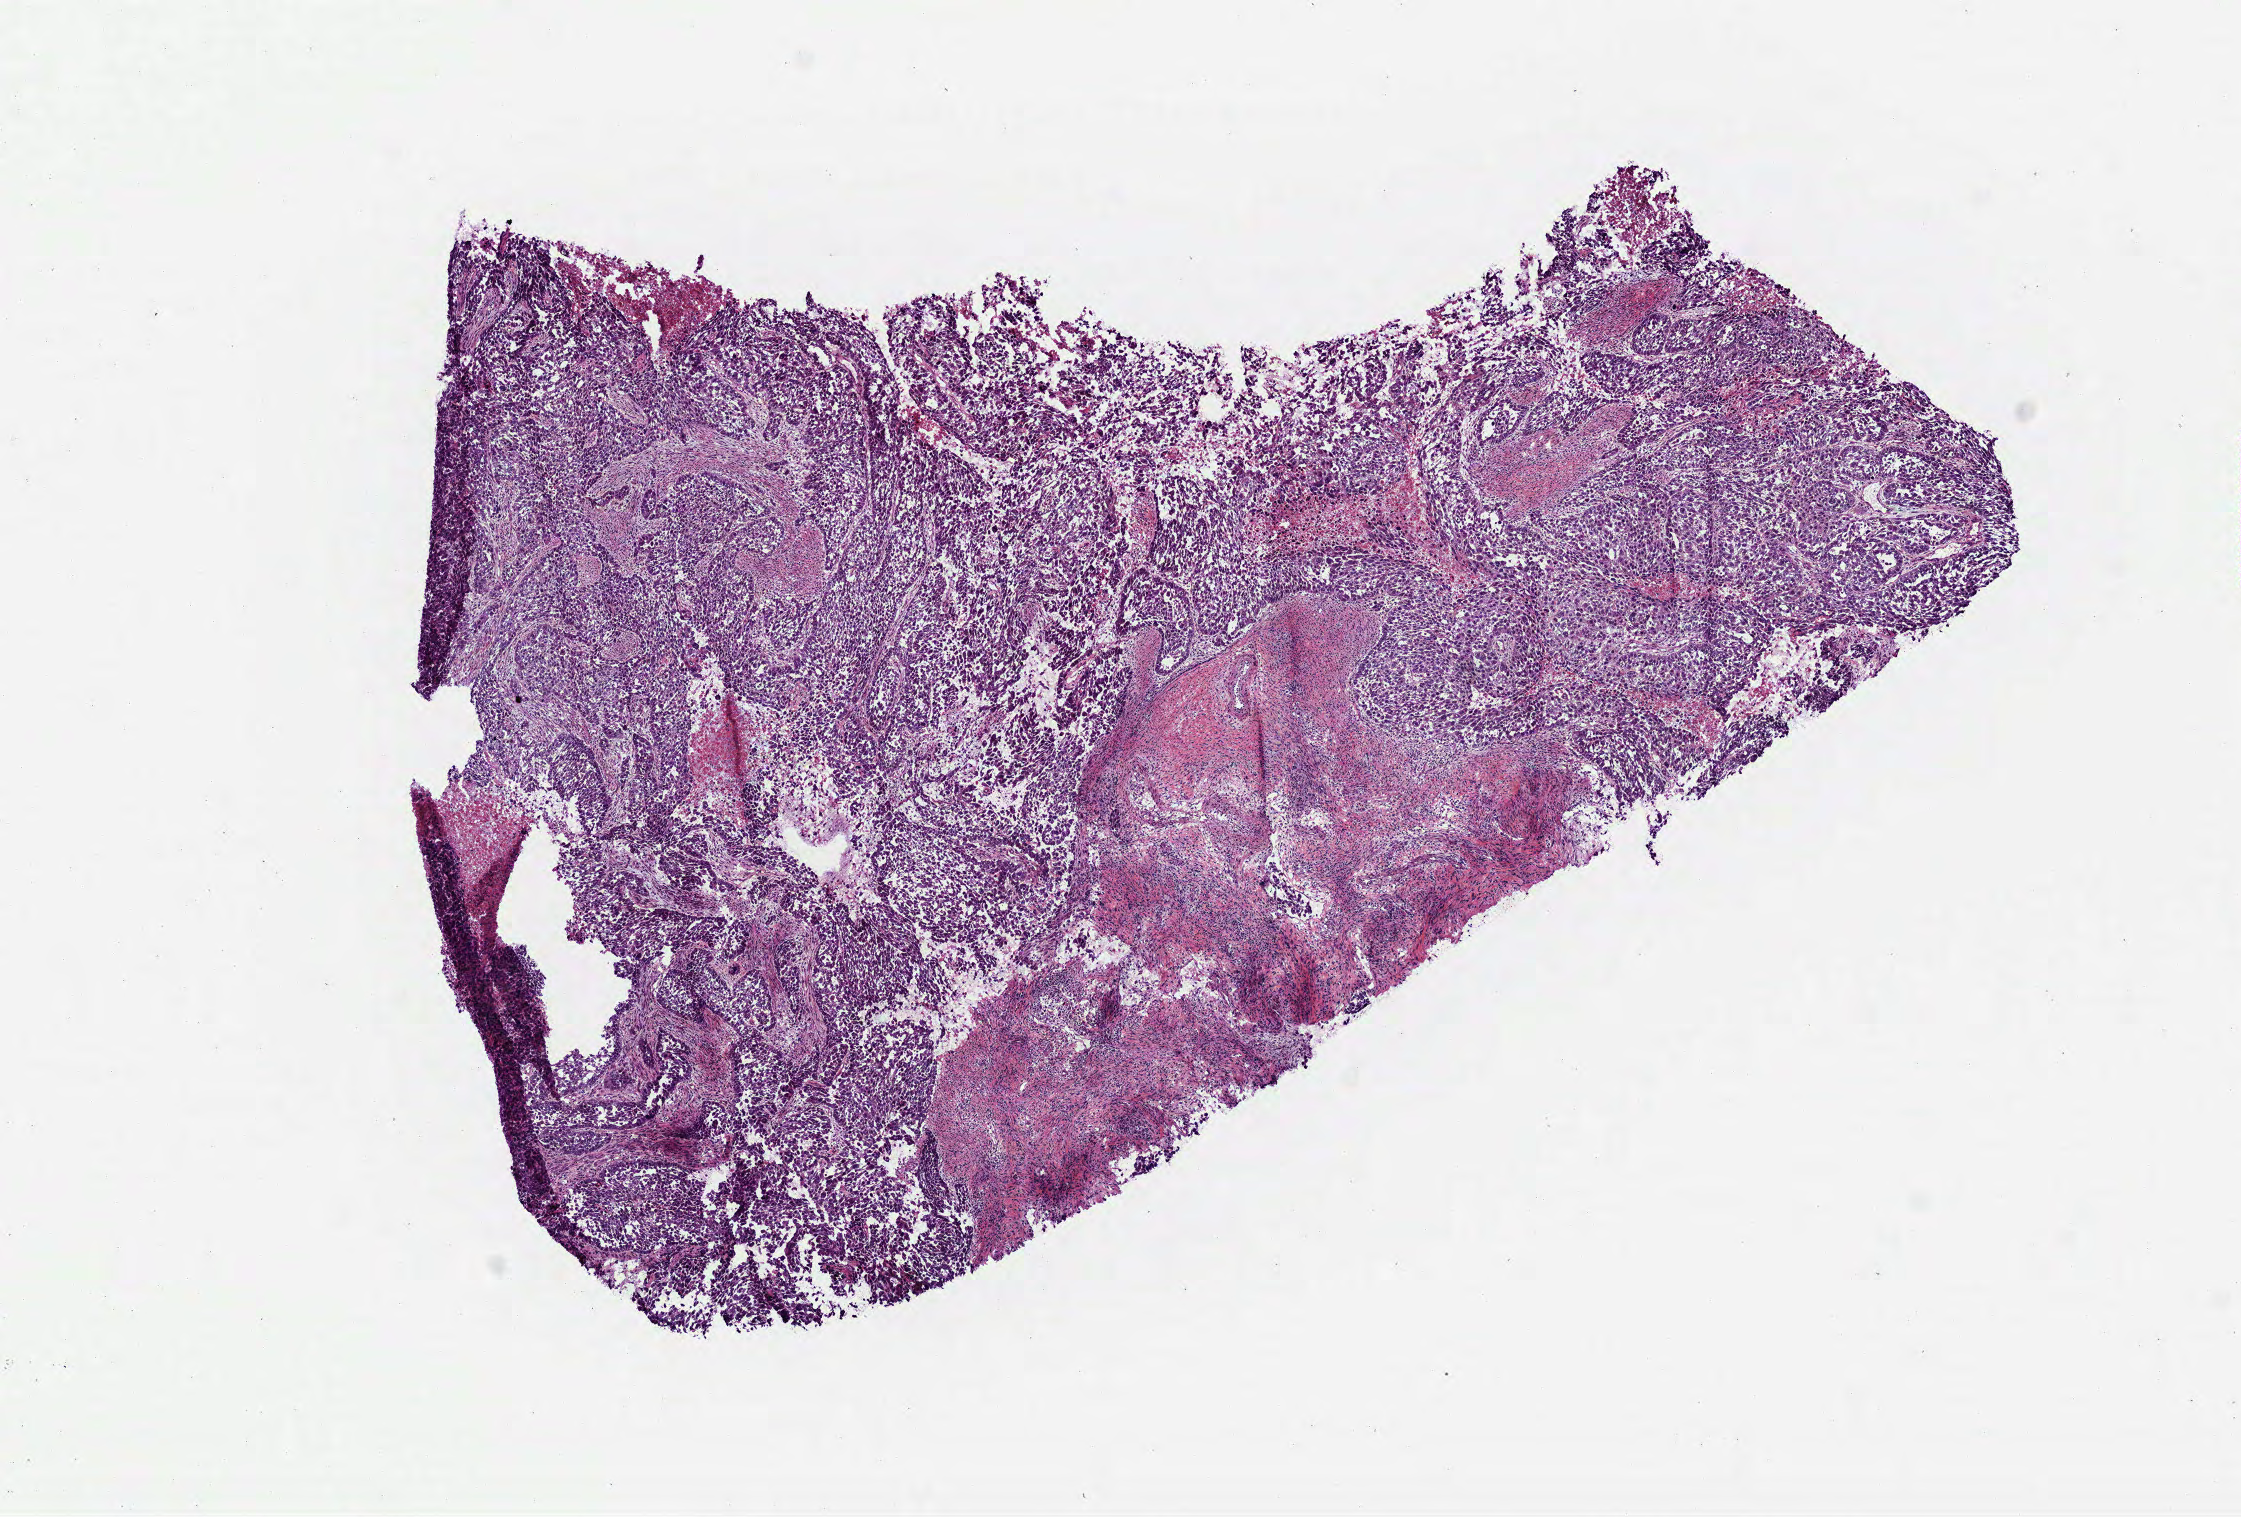
Whole-slide histology image, H&E-stained — whole scanned area (about 9.0 x 6.1 mm, slide scanned at 40x) shown as a low-resolution overview; frozen section from the top of the tissue portion; sample: primary tumour, lung. Male patient; age at initial diagnosis 68 years. Composition of this section per pathologist review: tumour cells 85%, tumour nuclei 80%, normal cells 0%, stromal cells 10%, necrosis 5%.
AJCC pathologic stage: IIB (6th edition). Histologic diagnosis: Squamous cell carcinoma, NOS.